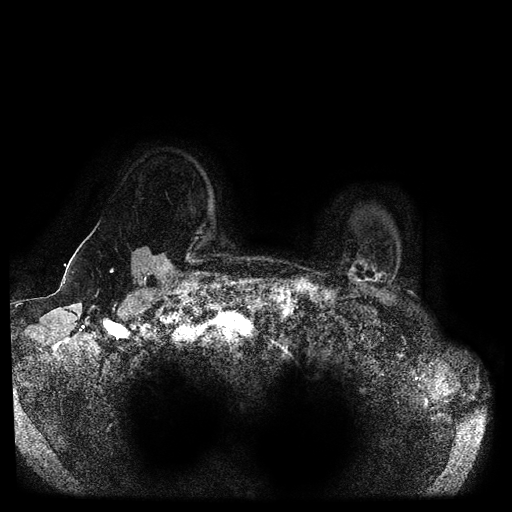
Breast MRI (dynamic contrast-enhanced, multi-phase), one axial slice. Dynamic contrast-enhanced series, time point 2 of 5 at this slice position (early post-contrast). 1.5 T. TE 2.6 ms, TR 5.3 ms. 2 mm slice thickness. 512 × 512 image matrix, field of view 370 × 370 mm. Patient: female, 55 years.
Annotated regions visible in this slice (semi-automatic segmentation, software-assisted and operator-edited):
- breast lesion (labelled benign in the annotation): box from (x=347, y=256) to (x=387, y=291) px